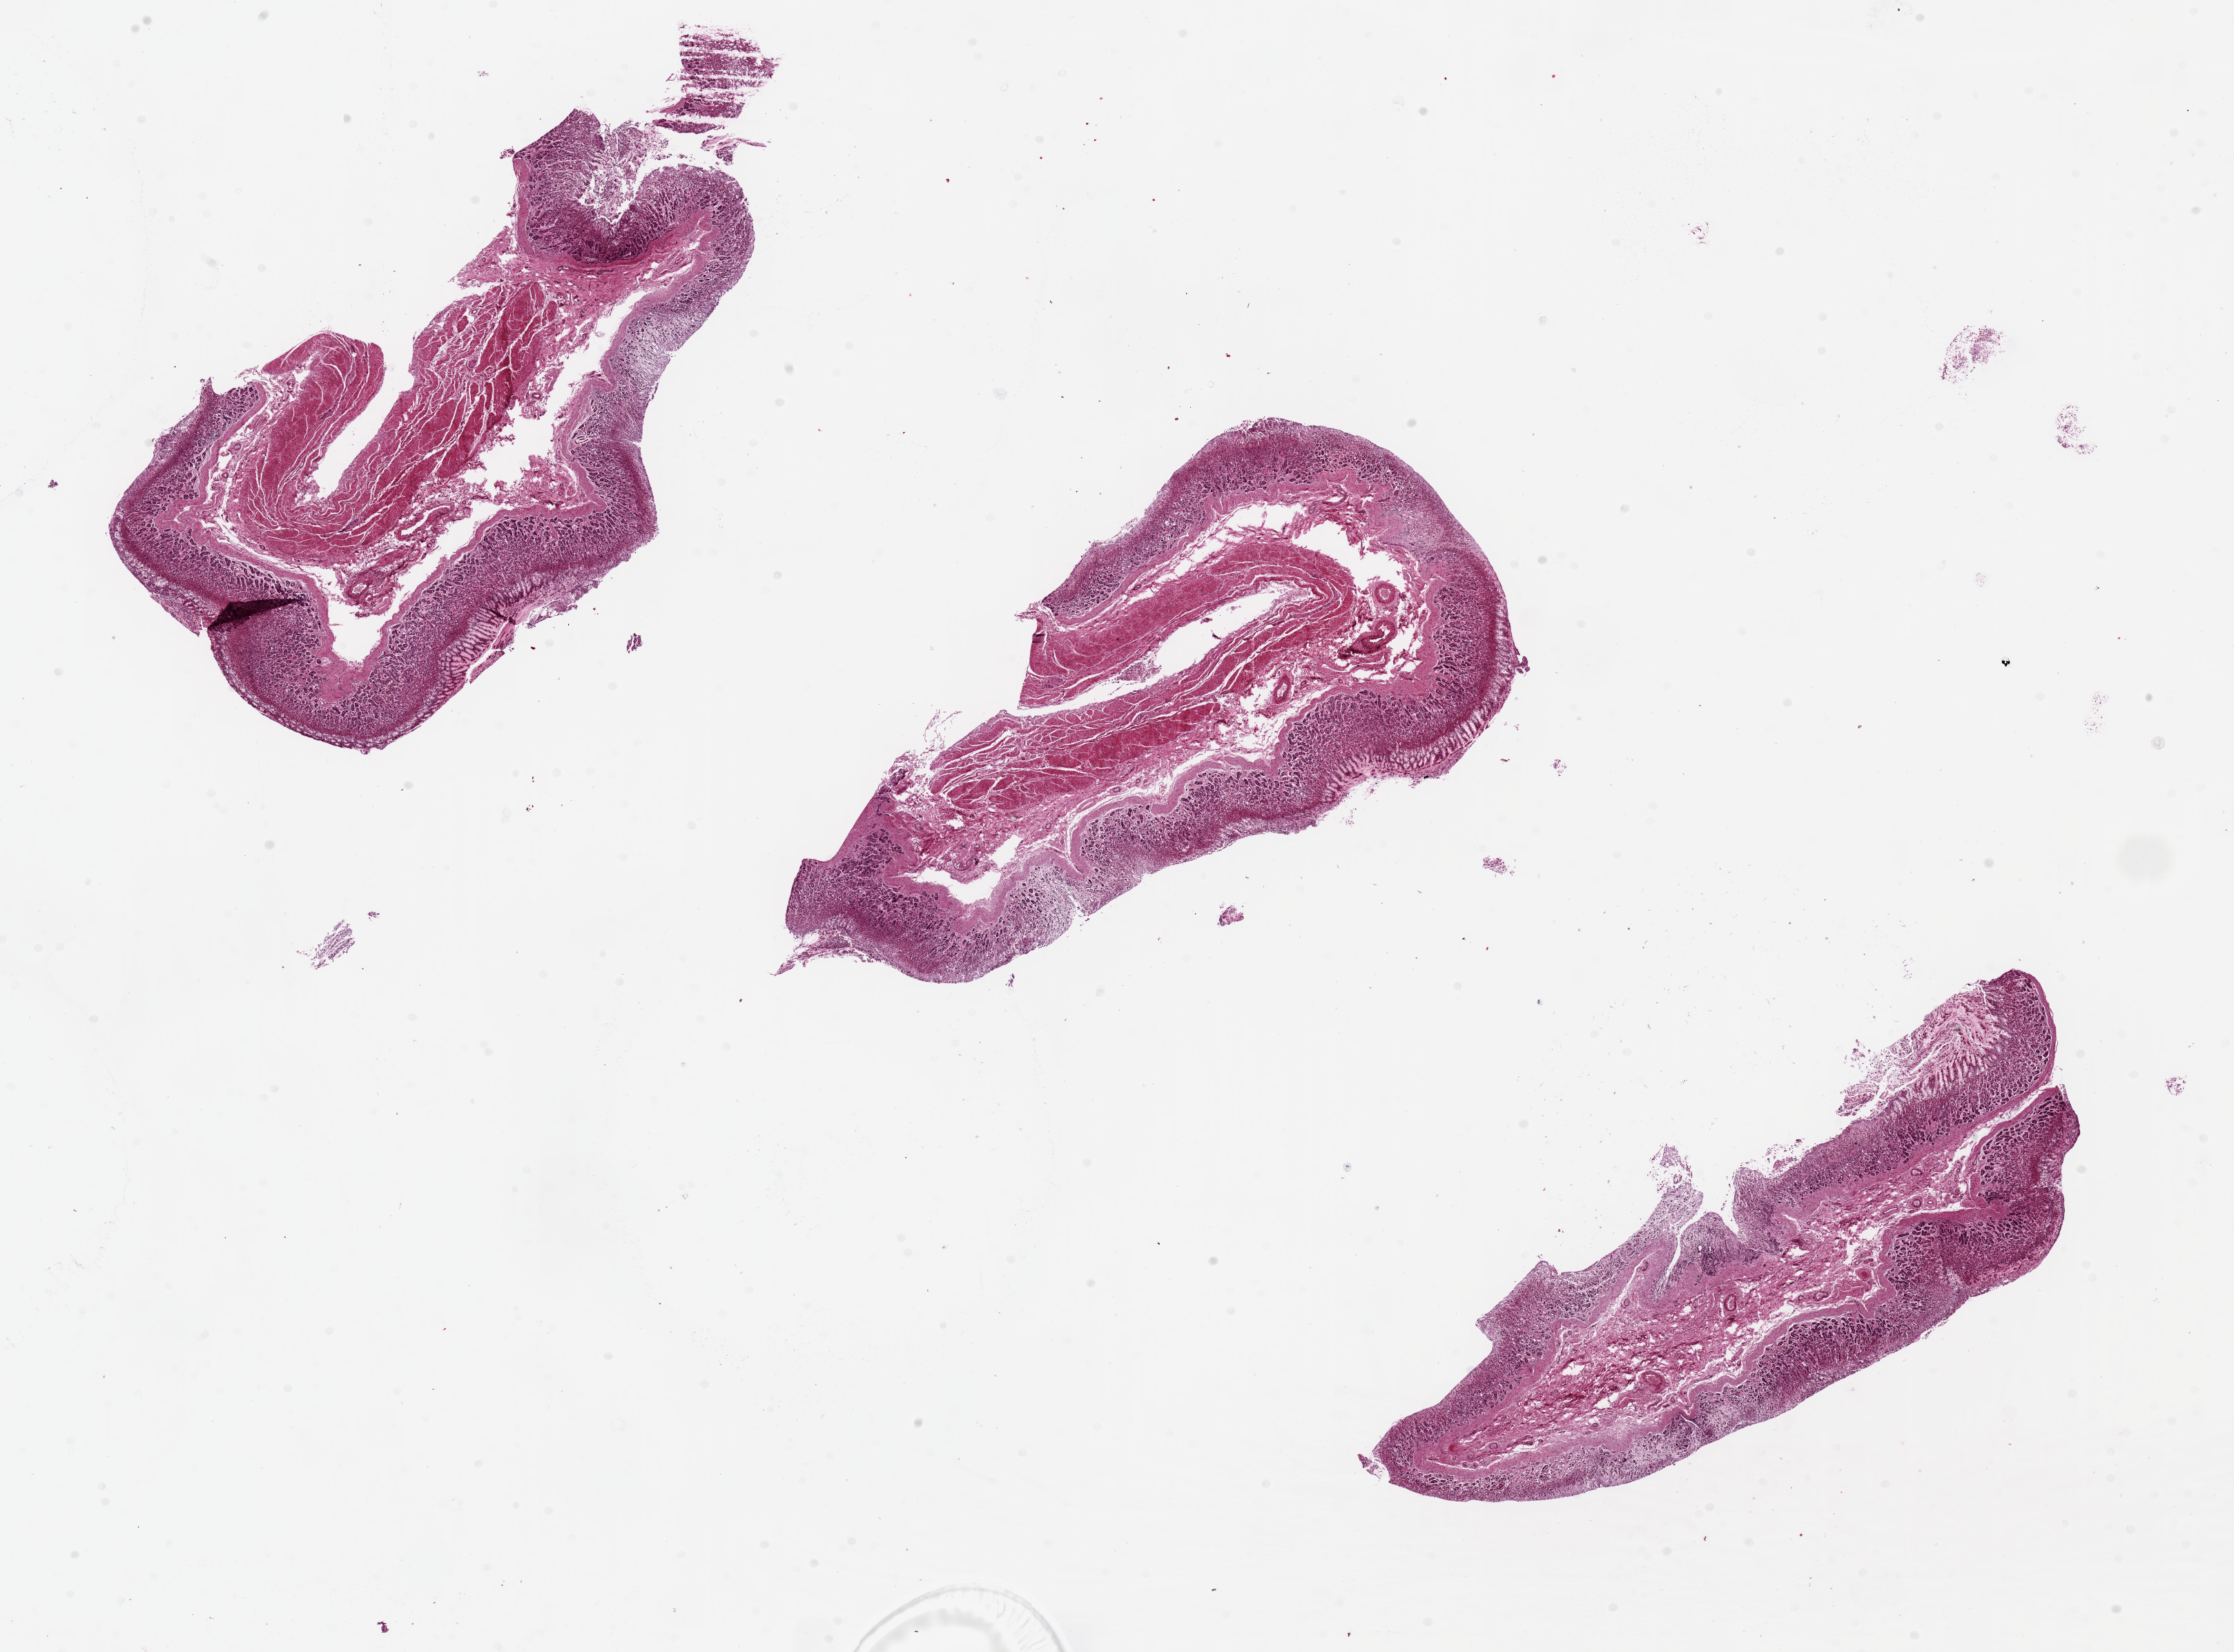
Haematoxylin and eosin whole-slide image, brightfield — shown as a low-resolution overview of the whole scanned area (about 25.6 x 18.9 mm, from a 20x scan). PAXgene-fixed, paraffin-embedded tissue. Target tissue: skeletal muscle. Tissue donor sample. Female donor.
Reviewer comment on this tissue sample: 7x1 mm.